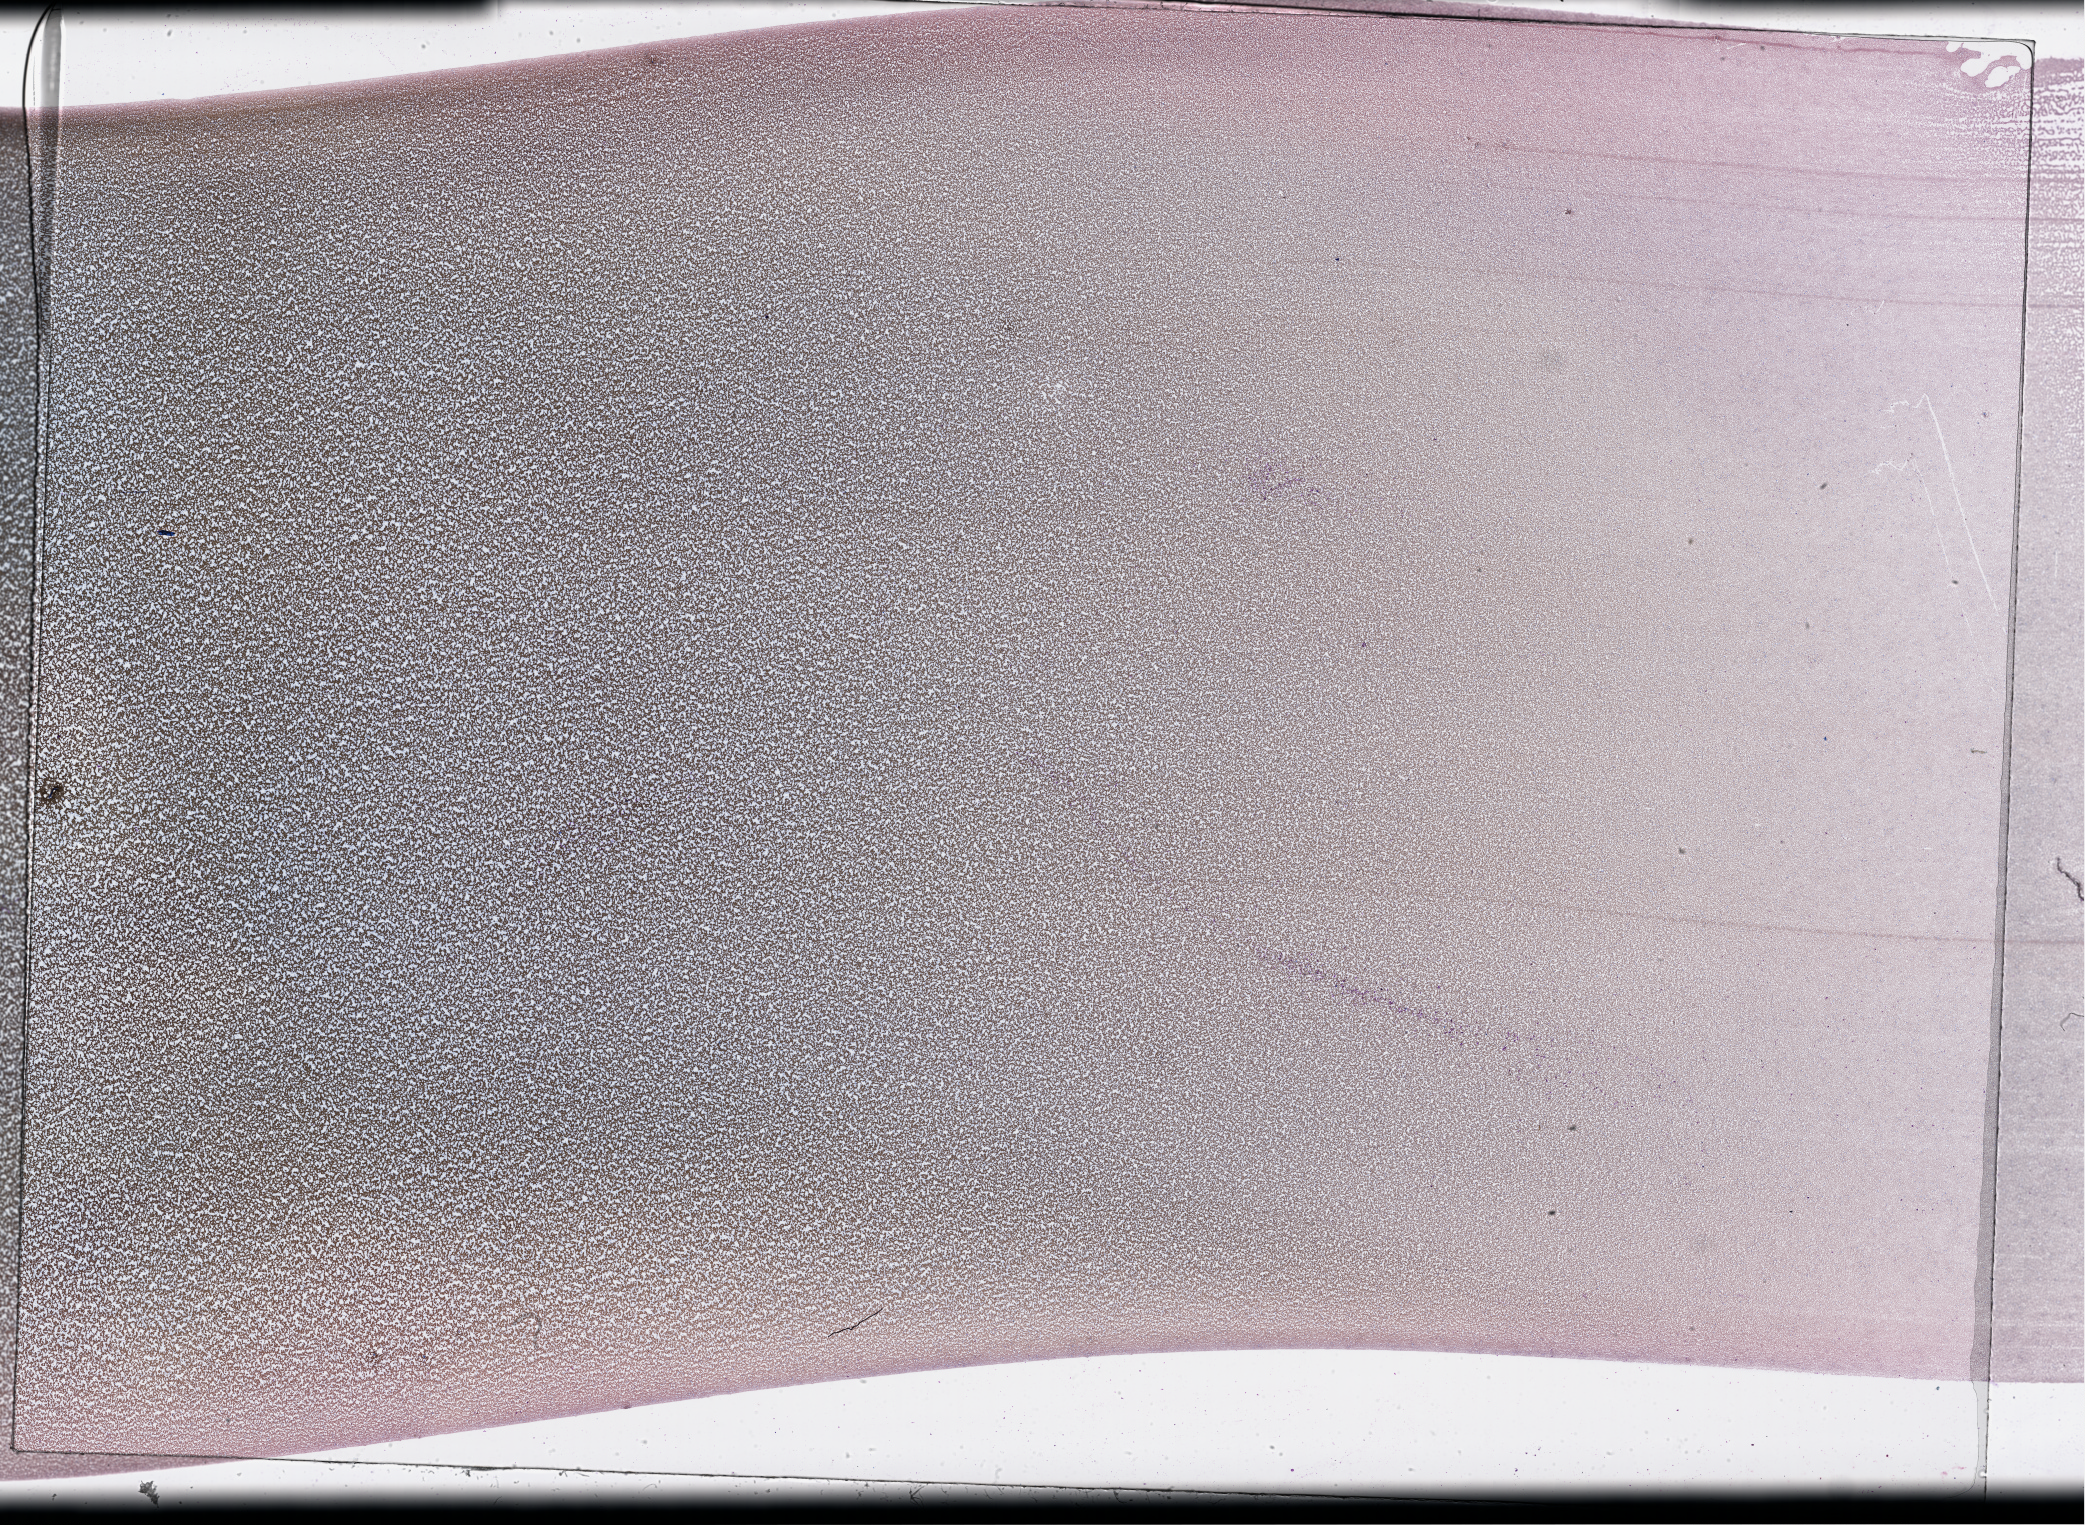
H&E-stained whole-slide image, whole scanned area (about 33.7 x 24.6 mm, slide scanned at 40x) shown as a low-resolution overview. Peripheral blood (leukaemic) sample. 69-year-old male patient.
- diagnosis: Acute Myeloid Leukemia
- FAB classification: M2